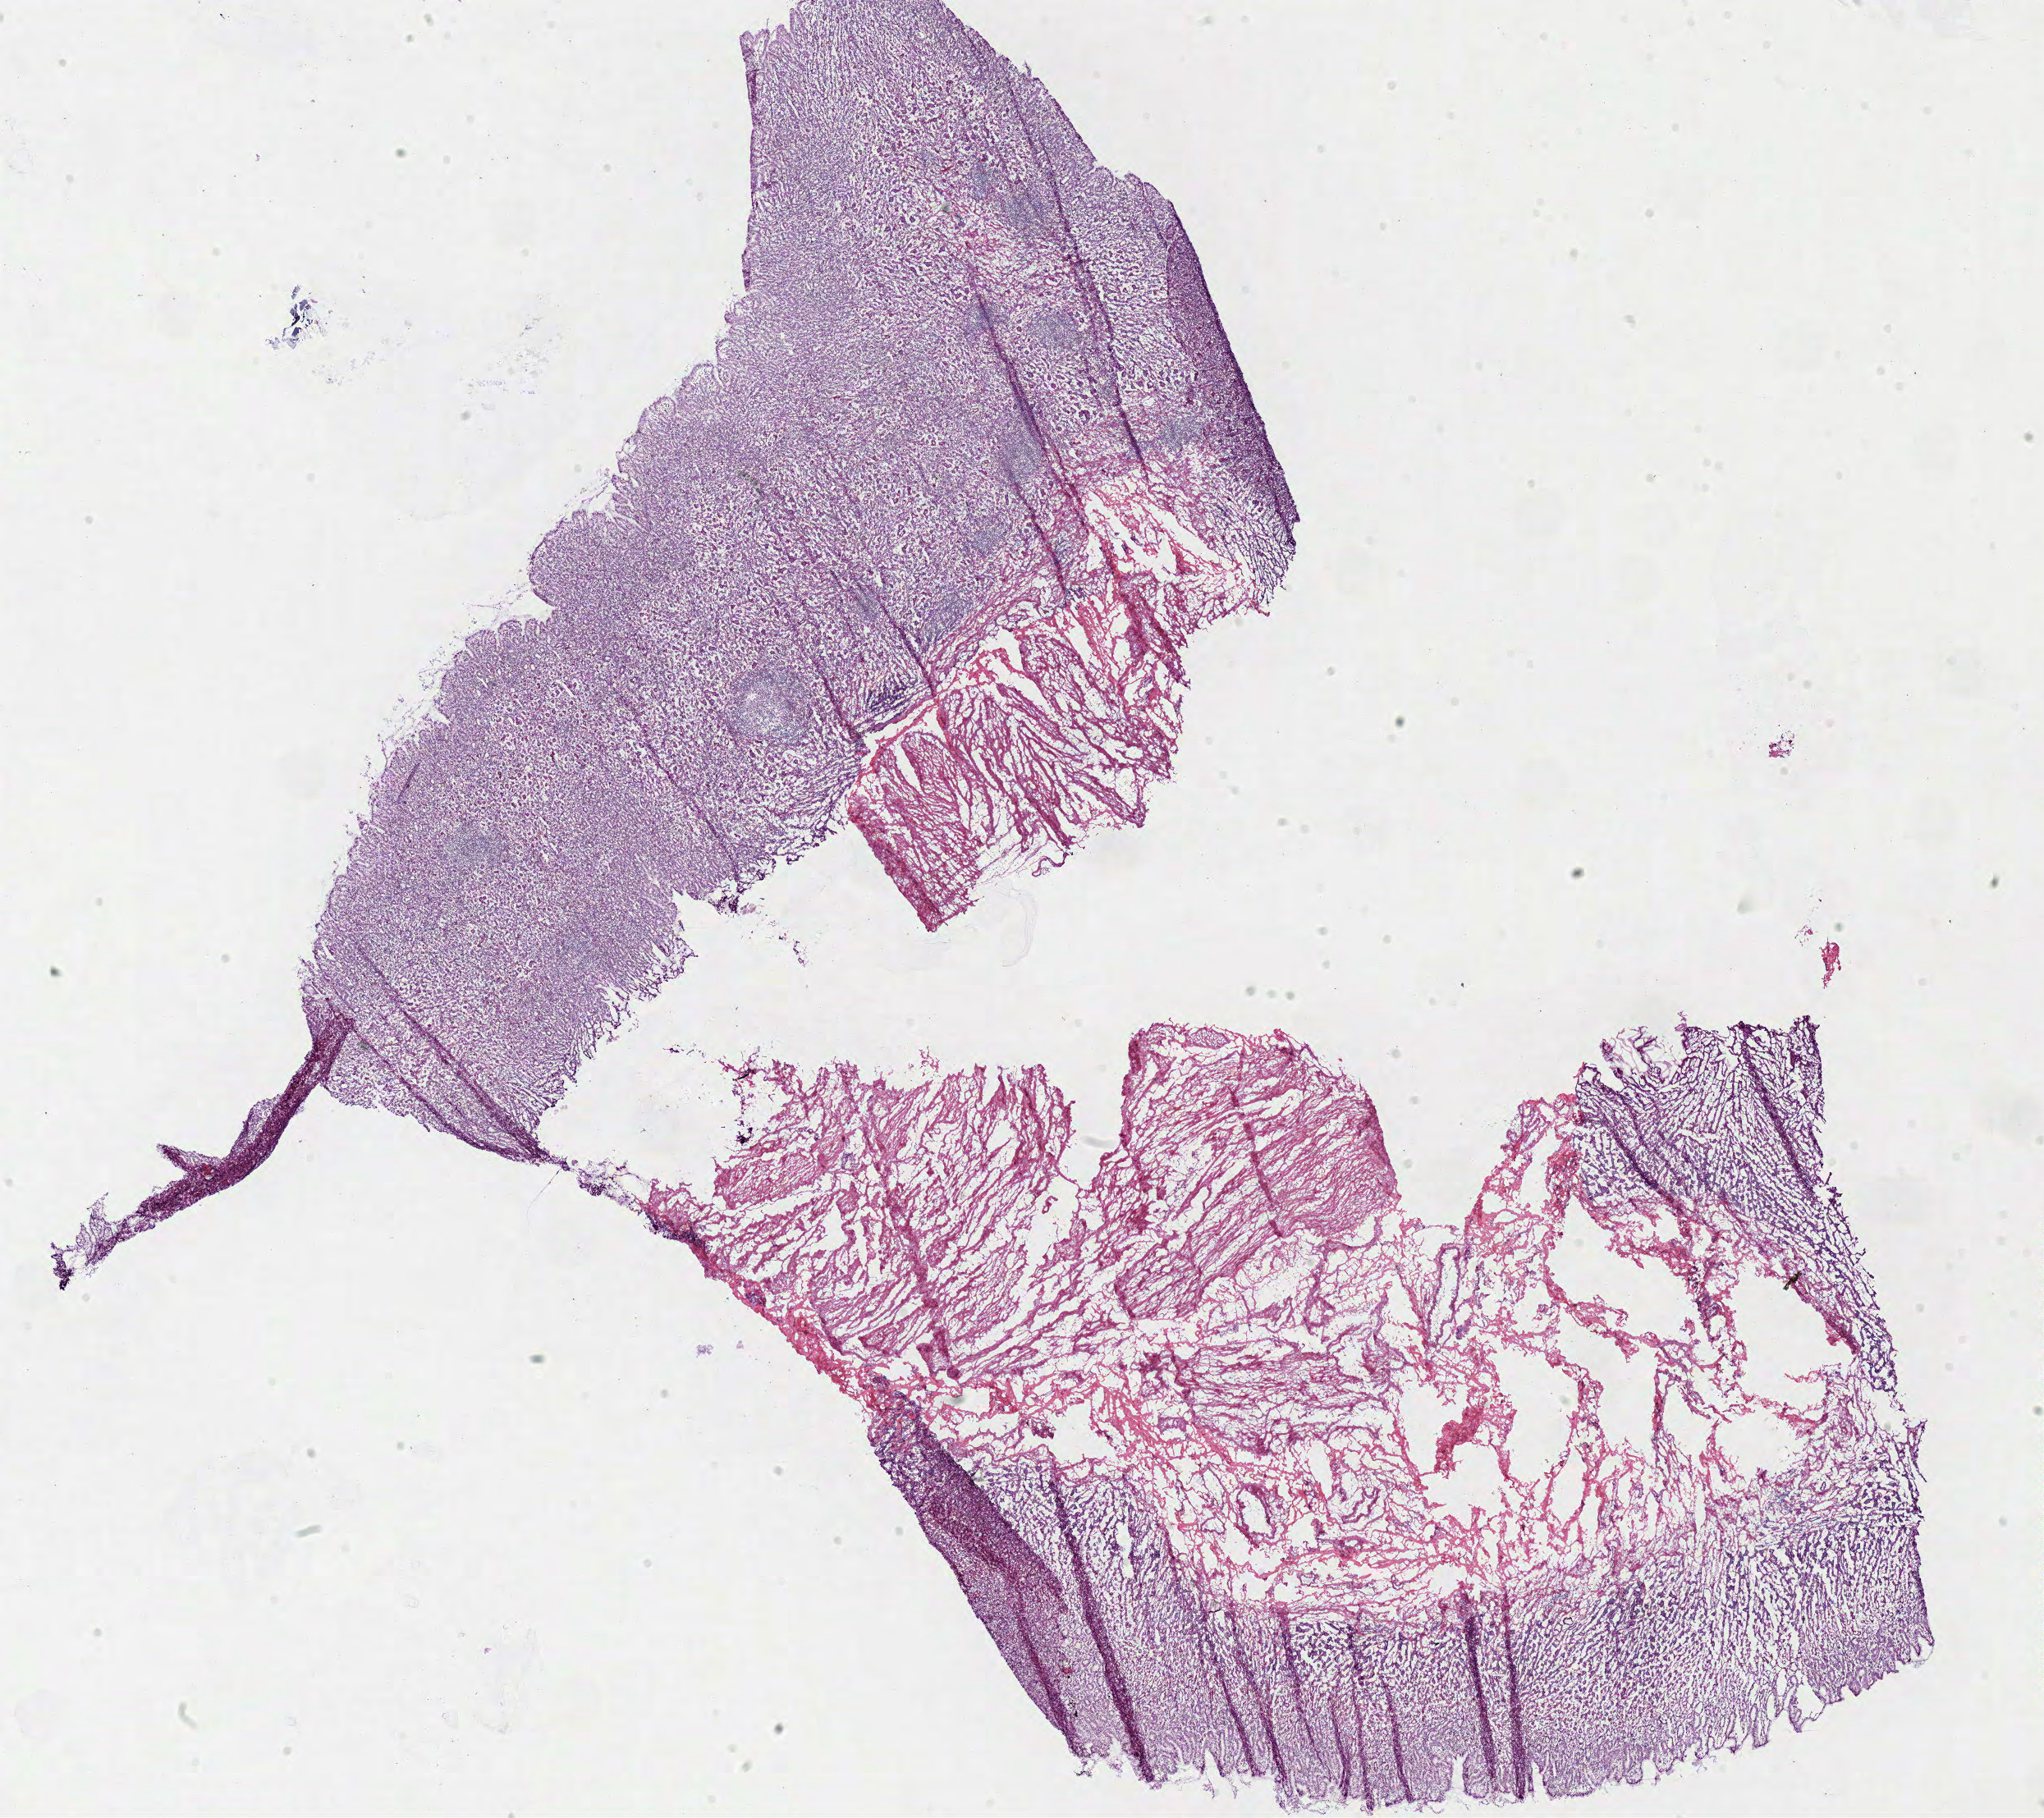
Whole-slide histology image, H&E-stained — shown as a low-resolution overview of the whole scanned area (about 19.6 x 17.4 mm). Frozen section. Sample: solid tissue normal (non-tumour tissue), stomach. Female patient; age at initial diagnosis 64 years.
This section: solid tissue normal (non-tumour) sample from the same patient. Patient diagnosis: Adenocarcinoma, NOS (body of stomach).